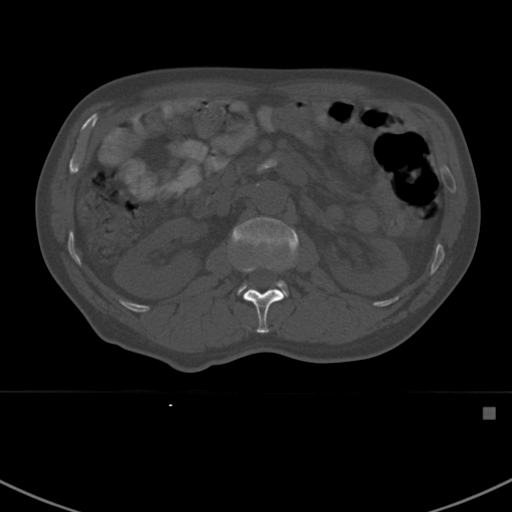
CT including the spine, one axial slice. Position 300 of 412 along the scan axis. Reconstruction kernel Br40s. Bone window (W 1800 / L 400 HU). 512 × 512 image matrix, field of view 358 × 358 mm. Patient: male, 59 years. From the clinical record (not read from this slice): primary cancer: prostate.
Structures marked on this image (semi-automatic segmentation, software-assisted and operator-edited):
- L1 vertebra: bounding box [x1, y1, x2, y2] px = [242, 264, 285, 334]
- L2 vertebra: [230, 217, 299, 297]